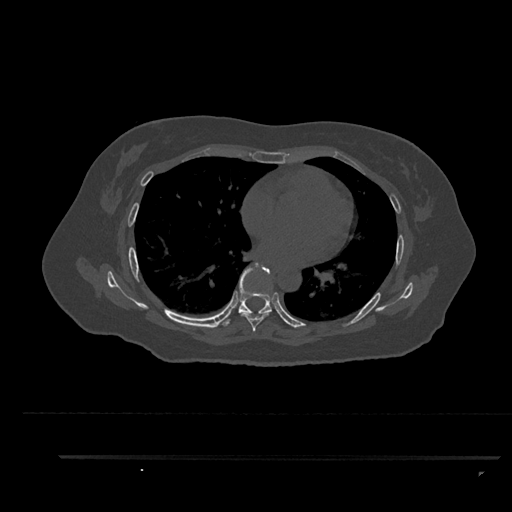
CT including the spine, one axial slice. Slice 533 of 797 in the series (ordered by position). 120 kVp. Bone window (W 1800 / L 400 HU). 0.5 mm slice thickness. 512 × 512 image matrix, field of view 408 × 408 mm. Female patient, age 44 years. From the clinical record (not read from this slice): primary cancer: renal; vertebrae with lytic lesions (as recorded): L1.
Structures marked on this image (semi-automatic segmentation, software-assisted and operator-edited):
- T6 vertebra: bounding box <241,312,271,333> (left, top, right, bottom; pixels)
- T7 vertebra: <223,262,272,326>